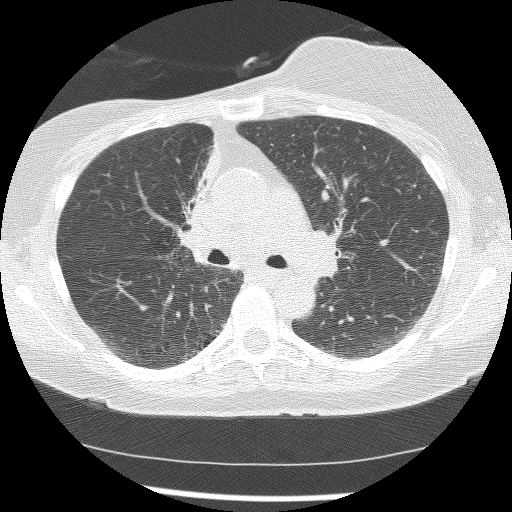
Low-dose screening chest CT, axial slice, first (baseline) screen, lung window (W 1500 / L -600 HU), 2.5 mm slice thickness, slice 60 of 172 in the series. Female, age 56 years at enrolment.
Expert-annotated lung lesion, bounding box <161,148,216,258> (left, top, right, bottom; pixels). The screening reader recorded 2 non-calcified nodules or masses ≥4 mm on this exam (right lower lobe, right middle lobe); which of them this box marks is not recorded. Later outcome: lung cancer diagnosed 1185 days after this screen (after the third annual screen) — adenocarcinoma, NOS, right upper lobe, stage IIIB (AJCC 6th edition), 8 mm at pathology.